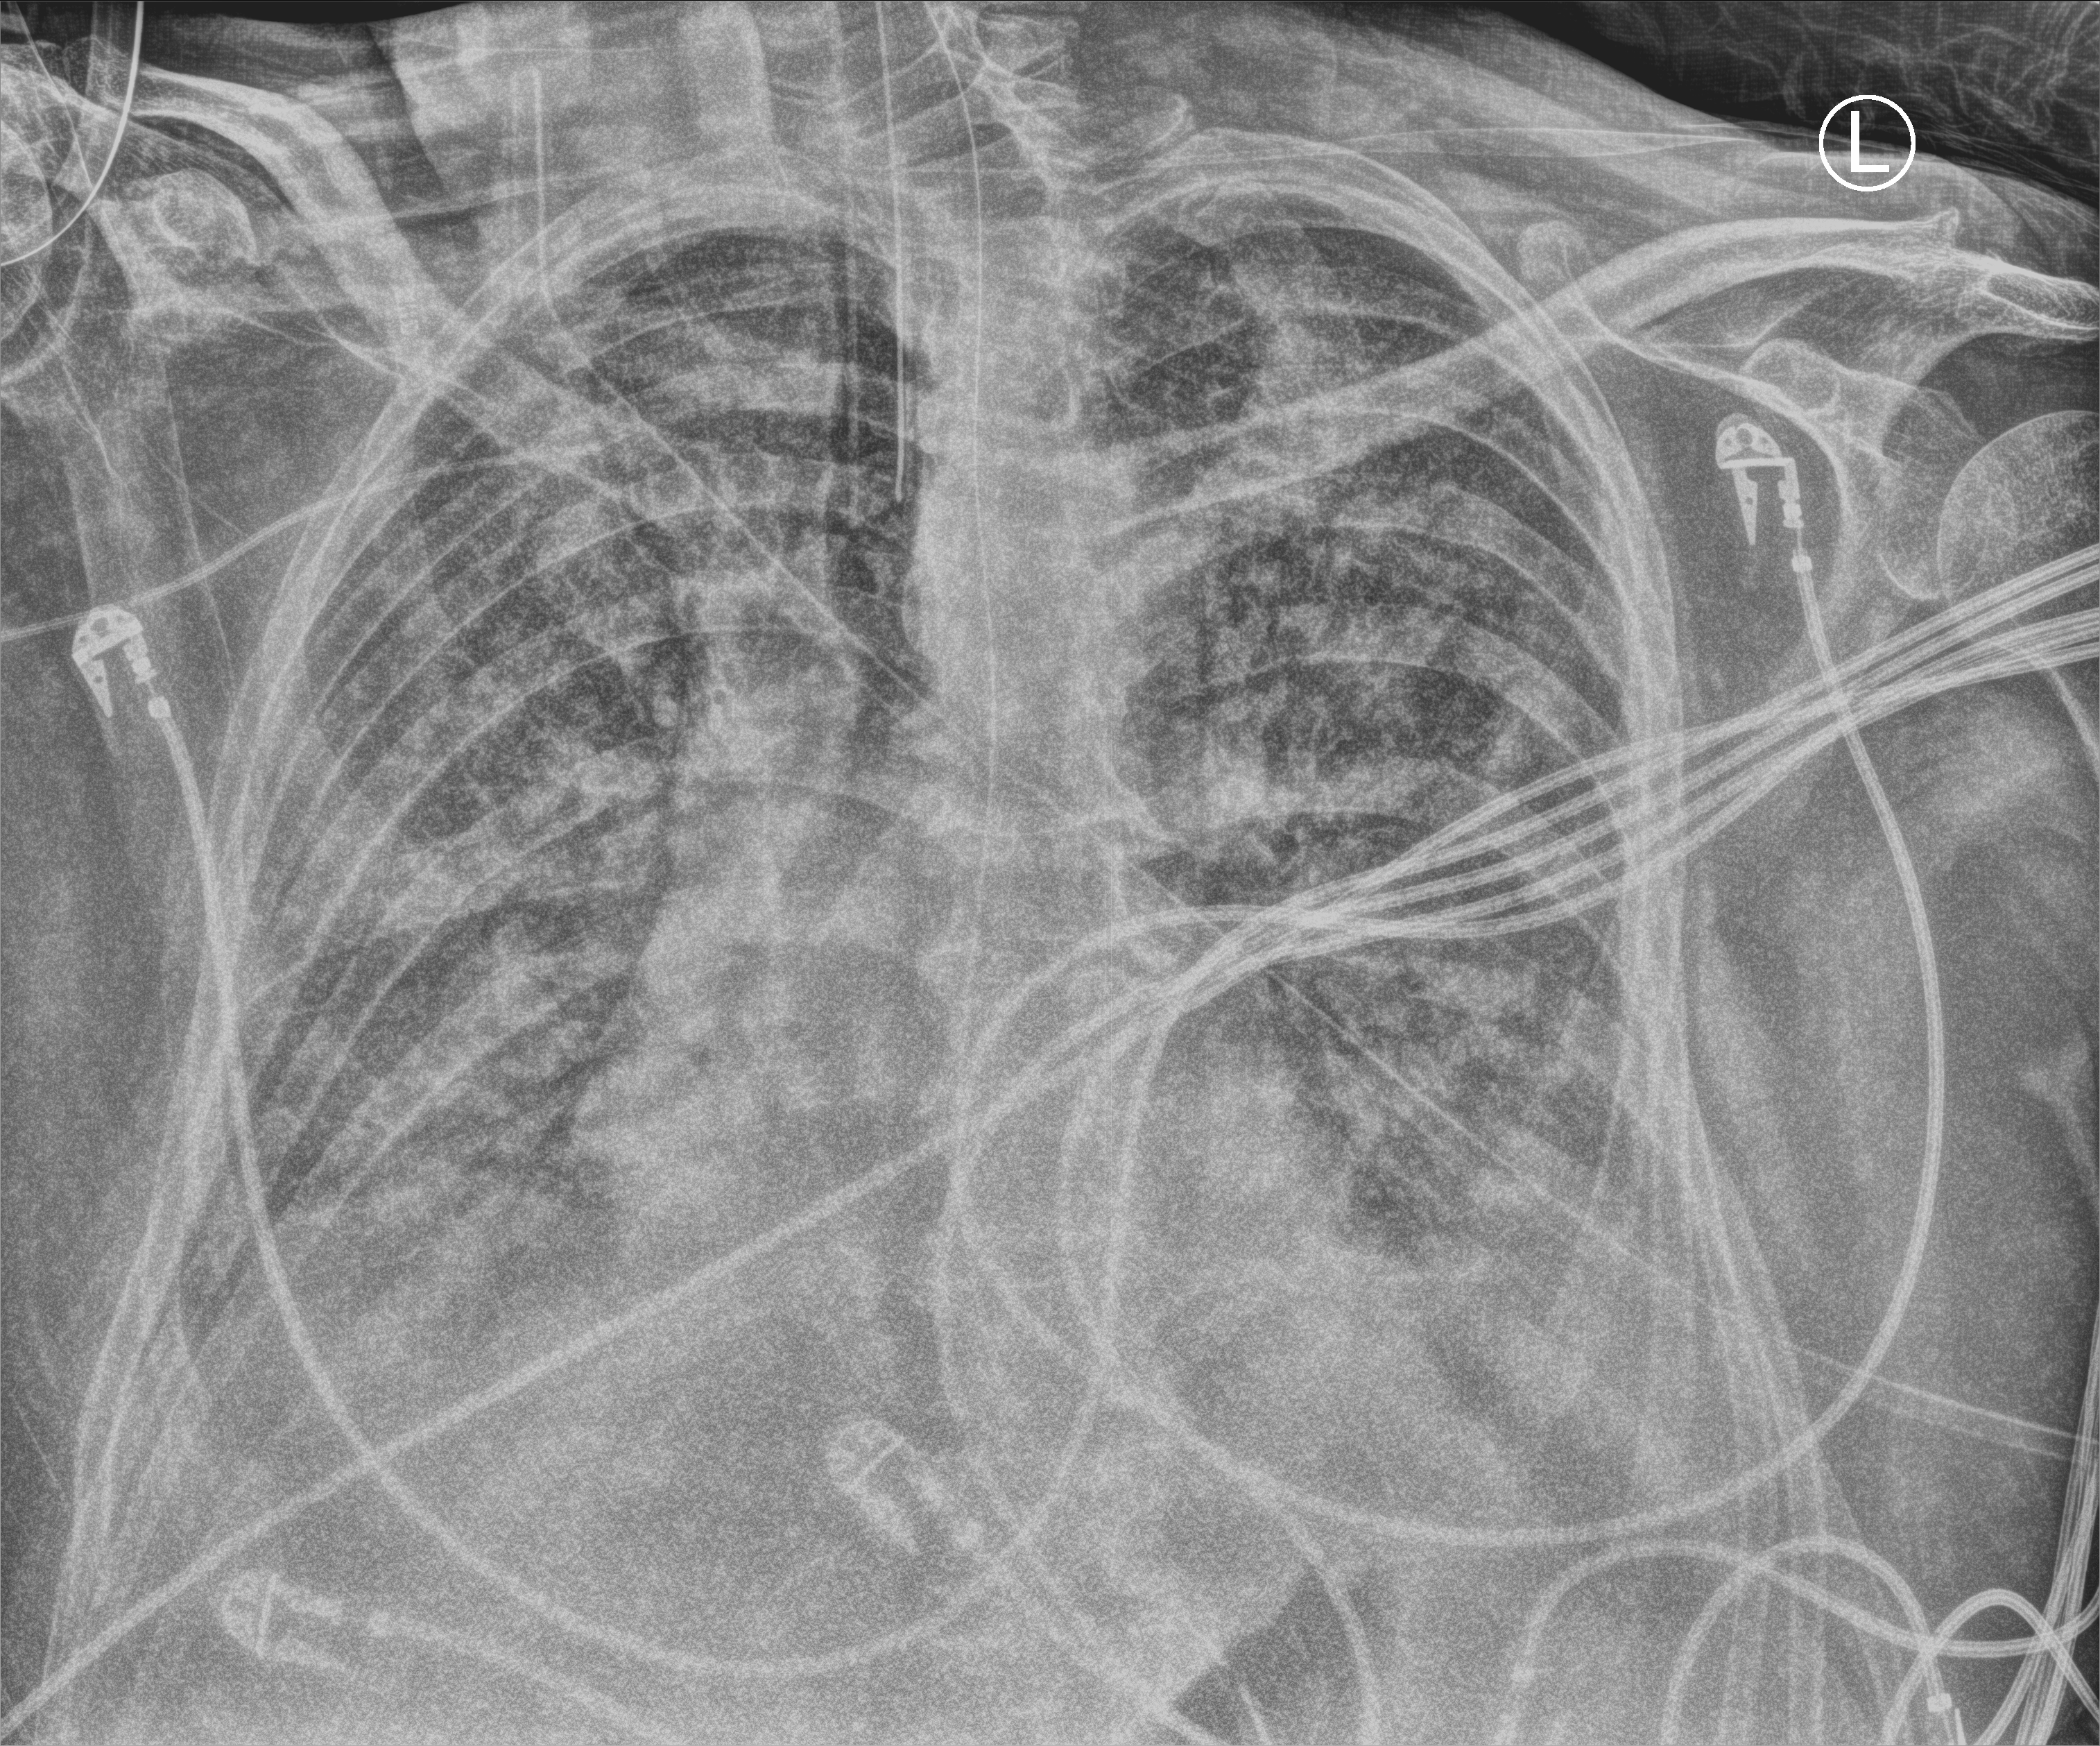
Bedside chest radiograph (computed radiography); anteroposterior (AP) projection. Patient hospitalised with COVID-19; male, aged 60–74 years.
Admission-level facts for this patient (not findings on this image; timing relative to this image not recorded):
- admitted to intensive care during this hospital stay: yes
- mechanically ventilated during this hospital stay: yes